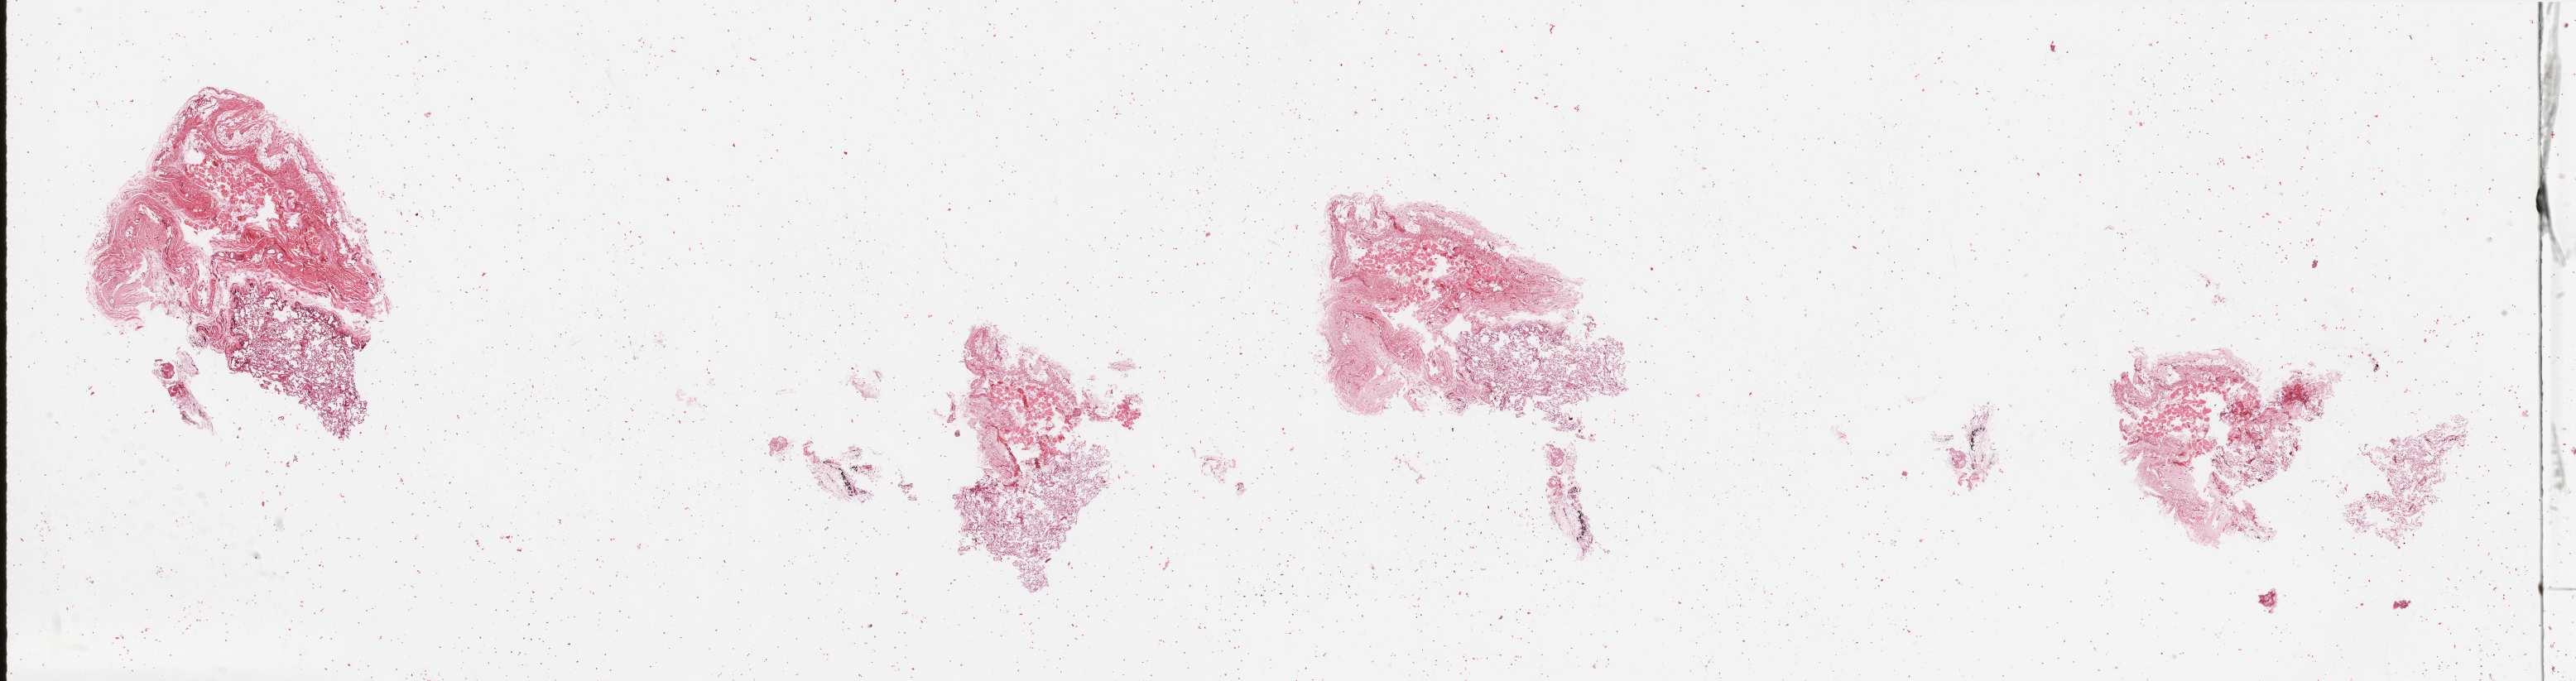
H&E whole-slide image — whole scanned area (about 49.2 x 13.0 mm, slide scanned at 20x) shown as a low-resolution overview. Normal (non-tumour) tissue sample, sampled site: lung. 51-year-old male patient.
This section: normal (non-tumour) tissue from the same patient. Patient diagnosis: Adenocarcinoma, NOS.